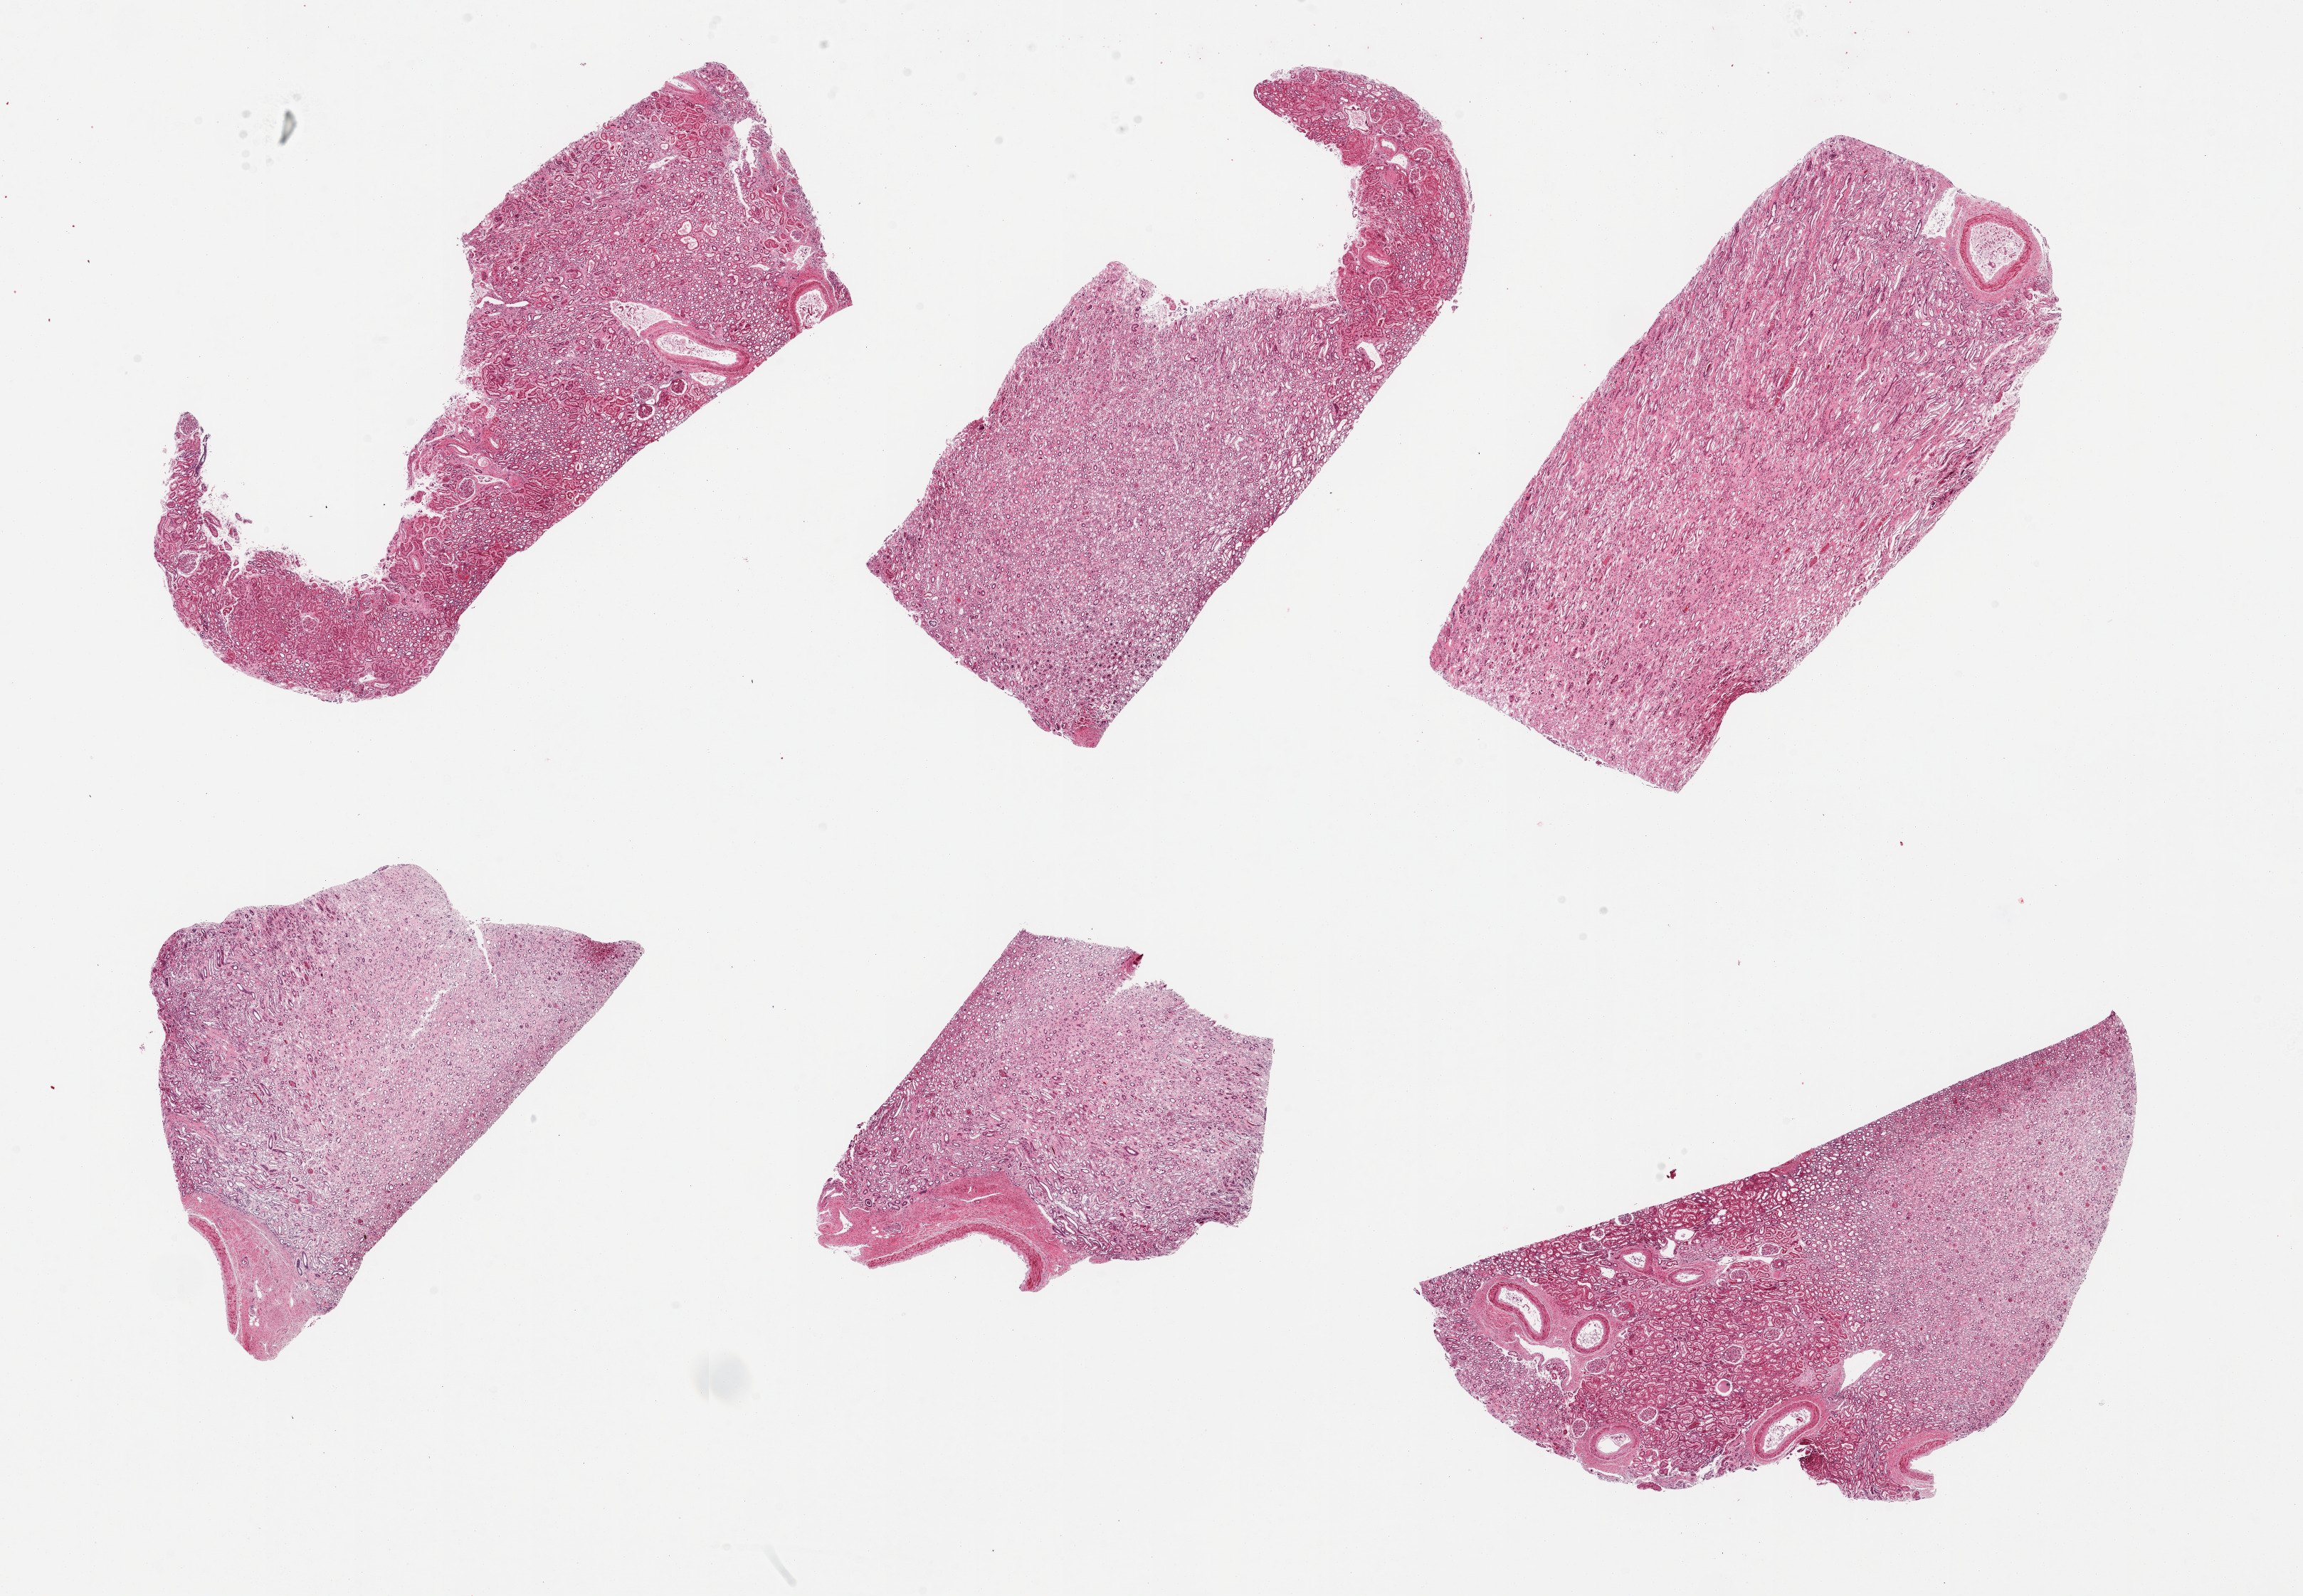
Whole-slide image, hematoxylin and eosin (H&E) stain, low-resolution overview of the scanned area, about 25.6 x 17.7 mm (slide scanned at 20x), PAXgene-fixed paraffin-embedded (PFPE) section, section of renal cortex (target tissue), tissue donor sample. Donor sex: male.
- reviewer comment on this tissue sample: 6 pieces; >90% medulla